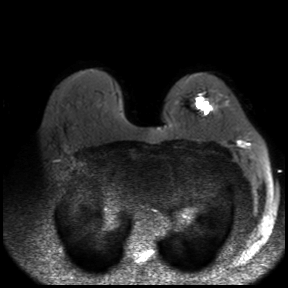
Breast MRI, one axial slice. Slice 21 of 30 in the series (ordered by position). Diffusion-weighted series; image 2 of 4 stored at this slice position (different b-values; order by instance number). 3 T. 4 mm slice thickness. 288 × 288 image matrix. Female patient.
Annotated regions visible in this slice (outlined manually by an expert reader):
- tumour on diffusion-weighted imaging: bounding box [x1, y1, x2, y2] px = [196, 97, 213, 115]